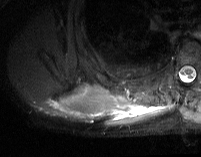
MRI of an extremity soft-tissue mass, one axial slice. Slice 17 of 74 in the series (ordered by position). STIR. MR volume resampled by the dataset authors to the PET/CT grid (not the native acquisition matrix). 3.27 mm slice thickness. 201 × 157 image matrix, field of view 196 × 153 mm. Male patient. From the clinical record (not read from this slice): histological type: pleiomorphic spindle cell undifferentiated; grade: high; site of the primary tumour: right parascapusular.
Outlined on this slice (expert contour drawn on MRI and transferred to this co-registered scan by the dataset authors):
- gross tumour volume including surrounding oedema: bounding box [x1, y1, x2, y2] px = [40, 84, 169, 126]
- gross tumour volume (mass): [71, 87, 105, 110]